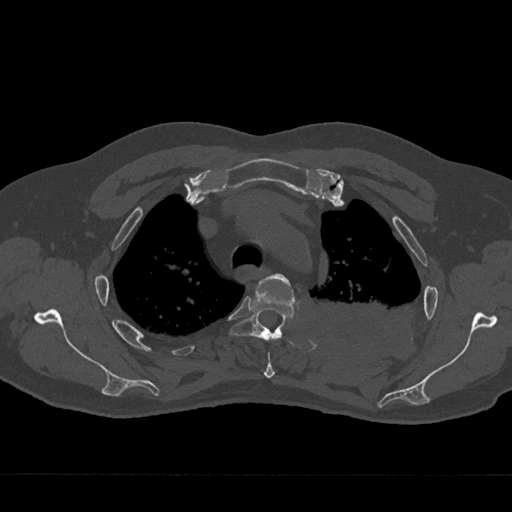
CT including the spine, one axial slice. Position 535 of 797 along the scan axis. 120 kVp. Bone window (W 1800 / L 400 HU). 512 × 512 image matrix. Patient: male, 75 years. Case-level facts recorded for this patient, not image findings: primary cancer: renal.
Annotated regions visible in this slice (semi-automatically segmented with operator editing):
- T3 vertebra: box from (x=261, y=274) to (x=293, y=379) px
- T4 vertebra: (x=229, y=284)–(x=296, y=341)